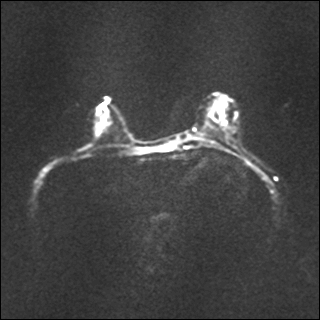
Breast MRI, one axial slice; slice 17 of 35 in the series (ordered by position); diffusion-weighted series; image 2 of 4 stored at this slice position (different b-values; order by instance number); 1.5 T; 4 mm slice thickness; 320 × 320 image matrix, field of view 320 × 320 mm. Female patient.
Annotated regions visible in this slice (manually delineated by an expert):
- tumour on diffusion-weighted imaging: bounding box <101,117,106,126> (left, top, right, bottom; pixels)